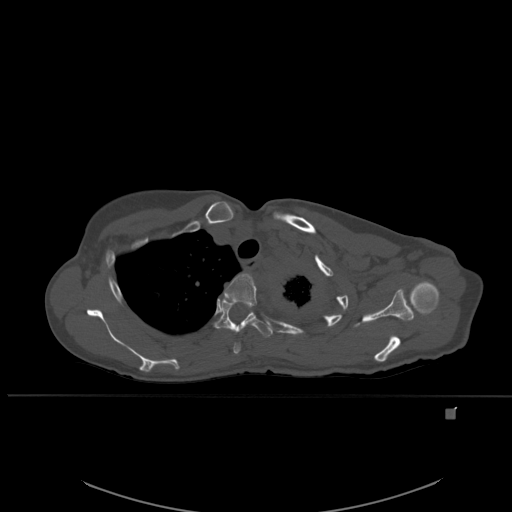
CT including the spine, one axial slice; slice 418 of 537 in the series (ordered by position); bone window (W 1800 / L 400 HU); 1.5 mm slice thickness; 512 × 512 image matrix. Patient: female, 45 years. Case-level facts recorded for this patient, not image findings: primary cancer: lung.
Annotated regions visible in this slice (semi-automatic segmentation, software-assisted and operator-edited):
- T3 vertebra: bounding box (x1, y1, x2, y2) in pixels: (224, 273, 258, 354)
- T4 vertebra: (214, 298, 273, 338)